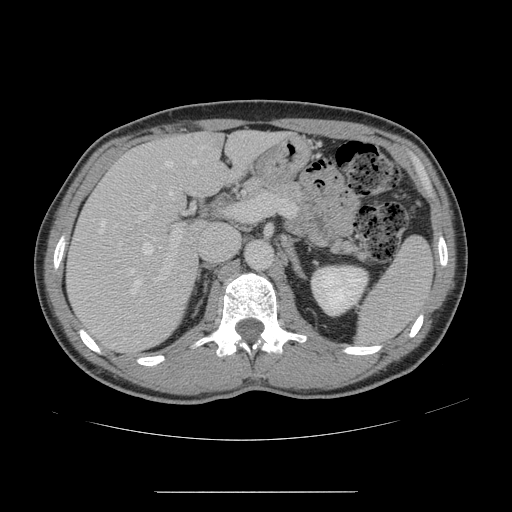
Contrast-enhanced abdominal CT, one axial slice; position 87 of 178 along the scan axis; 120 kVp; intravenous contrast given; soft-tissue window (W 400 / L 40 HU); 512 × 512 image matrix. Male patient, age 53 years. From the clinical record (not read from this slice): diagnosis: colorectal cancer liver metastases, imaged before liver resection.
Outlined on this slice (manually delineated by an expert):
- hepatic veins: bounding box (x1, y1, x2, y2) in pixels: (98, 160, 196, 295)
- liver: (68, 133, 279, 352)
- planned liver remnant (the part of the liver to remain after resection): (151, 132, 279, 195)
- portal vein (with intrahepatic branches): (134, 193, 267, 285)